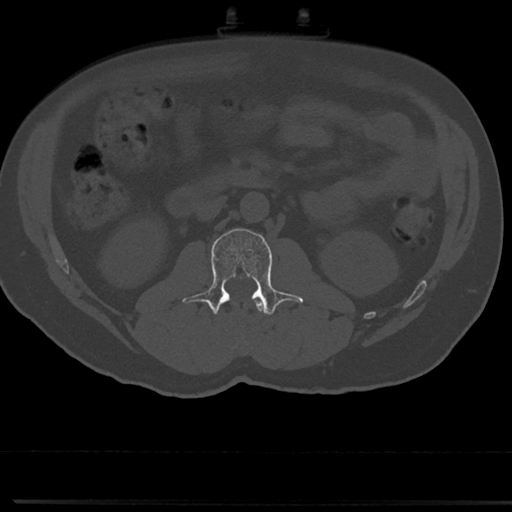
CT including the spine, one axial slice; slice 23 of 817 in the series (ordered by position); bone window (W 1800 / L 400 HU); 512 × 512 image matrix, field of view 355 × 355 mm. Patient: male, 61 years. From the clinical record (not read from this slice): primary cancer: prostate.
Structures marked on this image (semi-automatic segmentation, software-assisted and operator-edited):
- L1 vertebra: bounding box (x1, y1, x2, y2) in pixels: (238, 298, 263, 345)
- L2 vertebra: (191, 228, 302, 316)